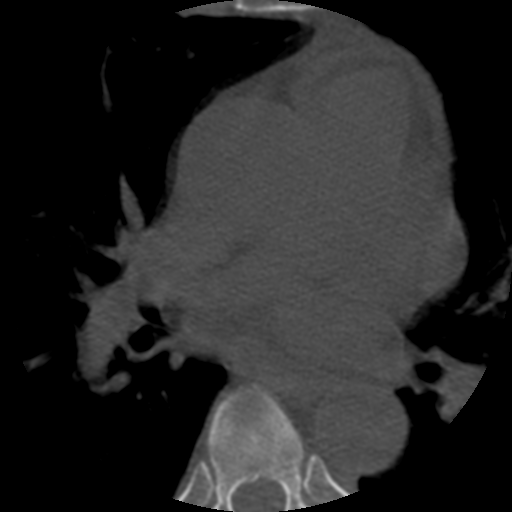
CT including the spine, one axial slice. 120 kVp. Bone window (W 1800 / L 400 HU). 1.25 mm slice thickness. 512 × 512 image matrix, field of view 160 × 160 mm. Patient age 57 years. Case-level facts recorded for this patient, not image findings: primary cancer: prostate.
Structures marked on this image (semi-automatically segmented with operator editing):
- T5 vertebra: box from (x=310, y=455) to (x=313, y=459) px
- T6 vertebra: (x=203, y=385)–(x=316, y=512)